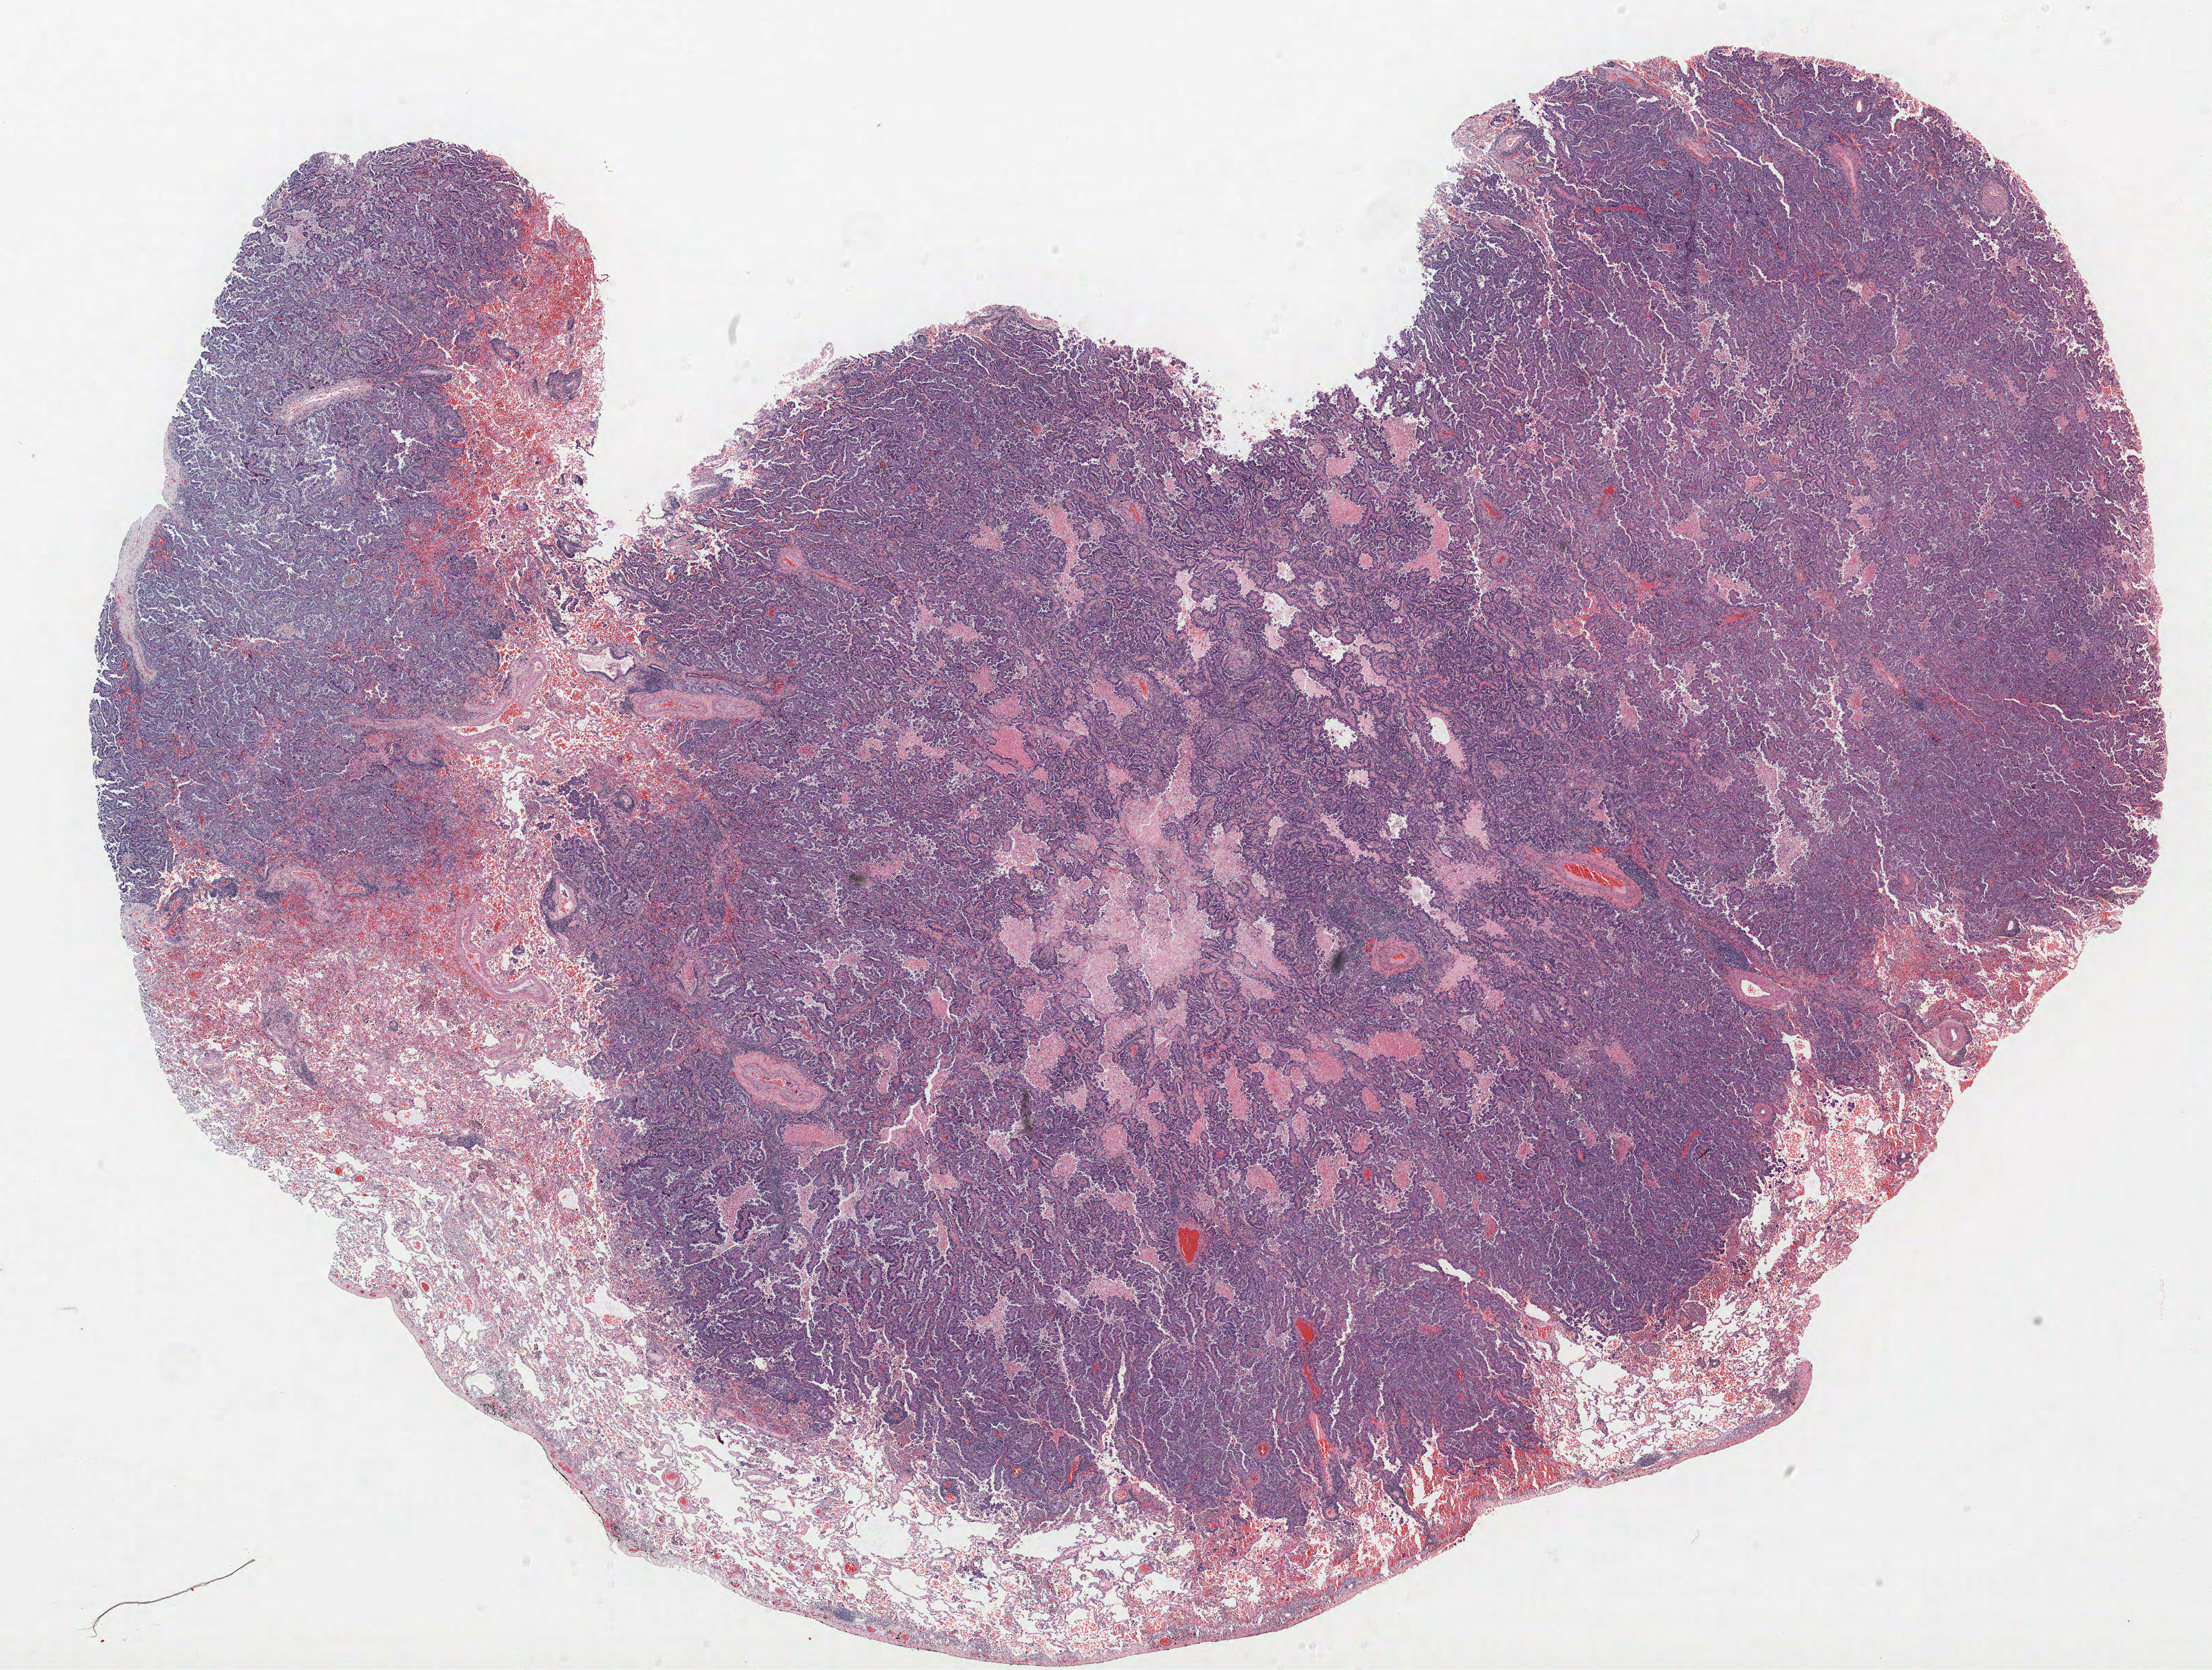
Hematoxylin and eosin (H&E) stained whole-slide image — whole scanned area (about 25.7 x 19.4 mm, acquisition: 40x scan) shown as a low-resolution overview; formalin-fixed paraffin-embedded (FFPE) section; lung. Male patient, aged 70 at enrolment. Current smoker at enrolment.
Primary tumour location (clinical record): left upper lobe. ICD-O-3 topography: upper lobe of lung (C34.1). Participant's lung-cancer diagnosis: Bronchiolo-alveolar adenocarcinoma, NOS (ICD-O-3 8250/3). Stage (AJCC 6th edition): IIIB. Tumour size (pathology): 25 mm.